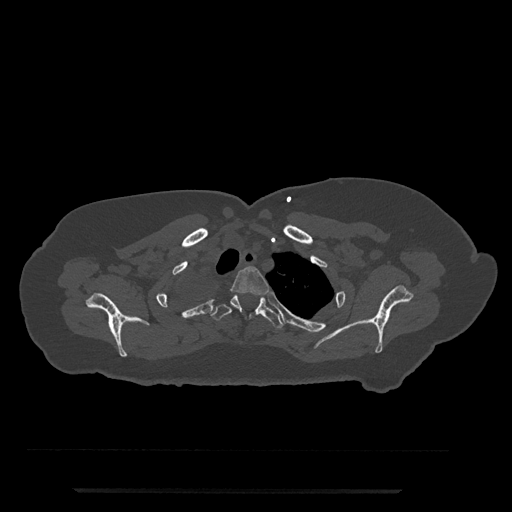
CT including the spine, one axial slice; slice 651 of 797 in the series (ordered by position); bone window (W 1800 / L 400 HU); 0.5 mm slice thickness; 512 × 512 image matrix. Patient: female, 51 years. From the clinical record (not read from this slice): primary cancer: neuro.
Outlined on this slice (semi-automatic segmentation, software-assisted and operator-edited):
- T2 vertebra: bounding box [x1, y1, x2, y2] px = [230, 266, 269, 295]
- T3 vertebra: [191, 295, 284, 329]